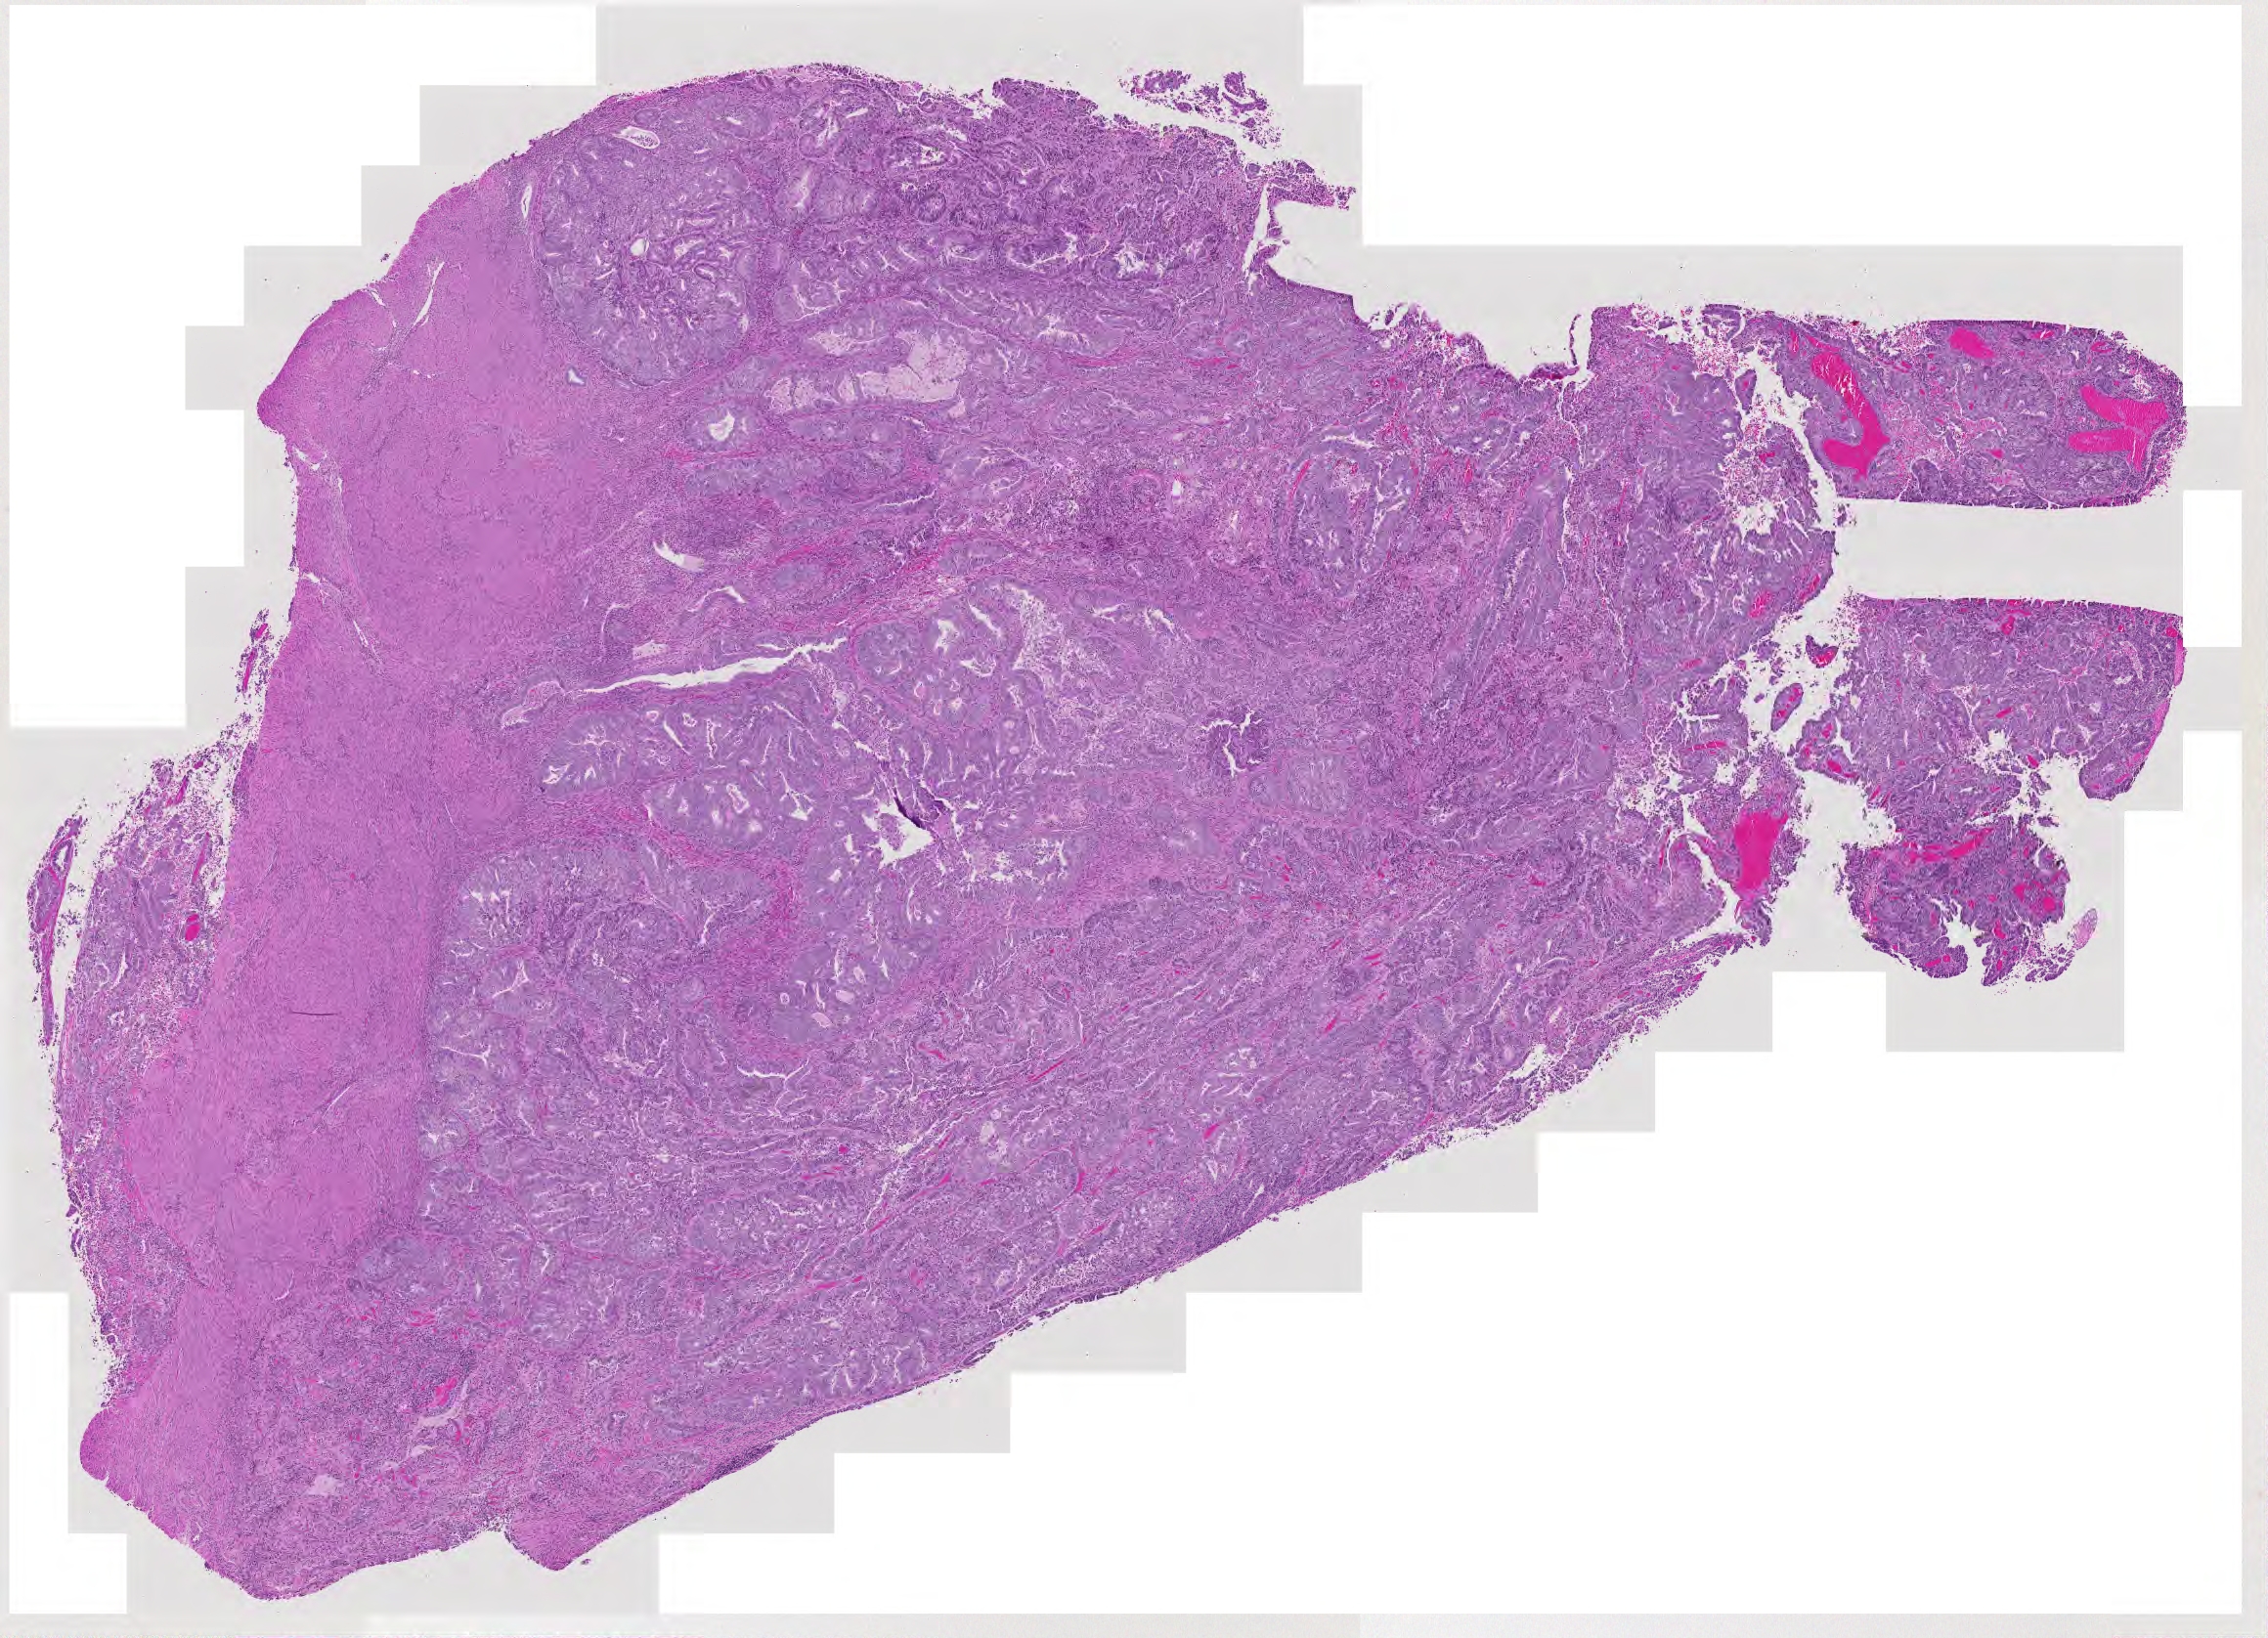
Digitized H&E tissue section (whole slide), whole scanned area (about 12.0 x 8.6 mm) shown as a low-resolution overview, tumour tissue sample, sampled site: uterus. Female, 54 y/o. Histologic grade: G2 (moderately differentiated). Slide review estimates, as recorded: tumour nuclei 80%, necrosis 2%.
- AJCC pathologic stage: I
- diagnosis: Endometrioid adenocarcinoma, NOS